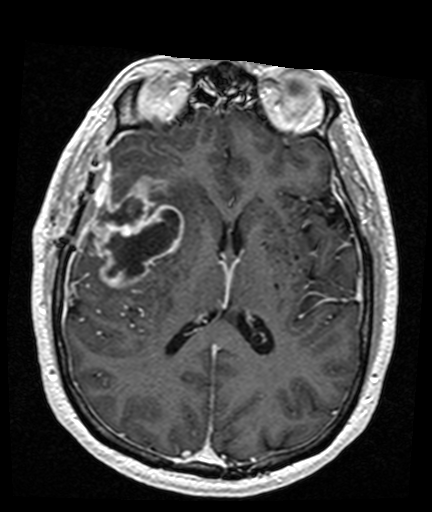
Brain MRI from a brain-tumour surgery series, one axial slice. Position 77 of 176 along the scan axis. T1-weighted post-contrast. 1 mm slice thickness. 432 × 512 image matrix. Case-level facts recorded for this patient, not image findings: histopathology: Glioblastoma; WHO grade: 4; IDH mutation: no; tumour location: Right Frontal Temporal, Posterior Sylvian Fissure.
Structures marked on this image (outlined manually by an expert reader):
- tumour: bounding box <92,176,183,290> (left, top, right, bottom; pixels)